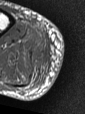
MRI of an extremity soft-tissue mass, one axial slice. Slice 9 of 47 in the series (ordered by position). MR volume resampled by the dataset authors to the PET/CT grid (not the native acquisition matrix). 85 × 114 image matrix, field of view 83 × 111 mm. Male patient. Case-level facts recorded for this patient, not image findings: histological type: pleiomorphic liposarcoma; grade: high; site of the primary tumour: right calf.
Outlined on this slice (expert contour drawn on MRI and transferred to this co-registered scan by the dataset authors):
- gross tumour volume including surrounding oedema: box from (x=33, y=51) to (x=43, y=63) px